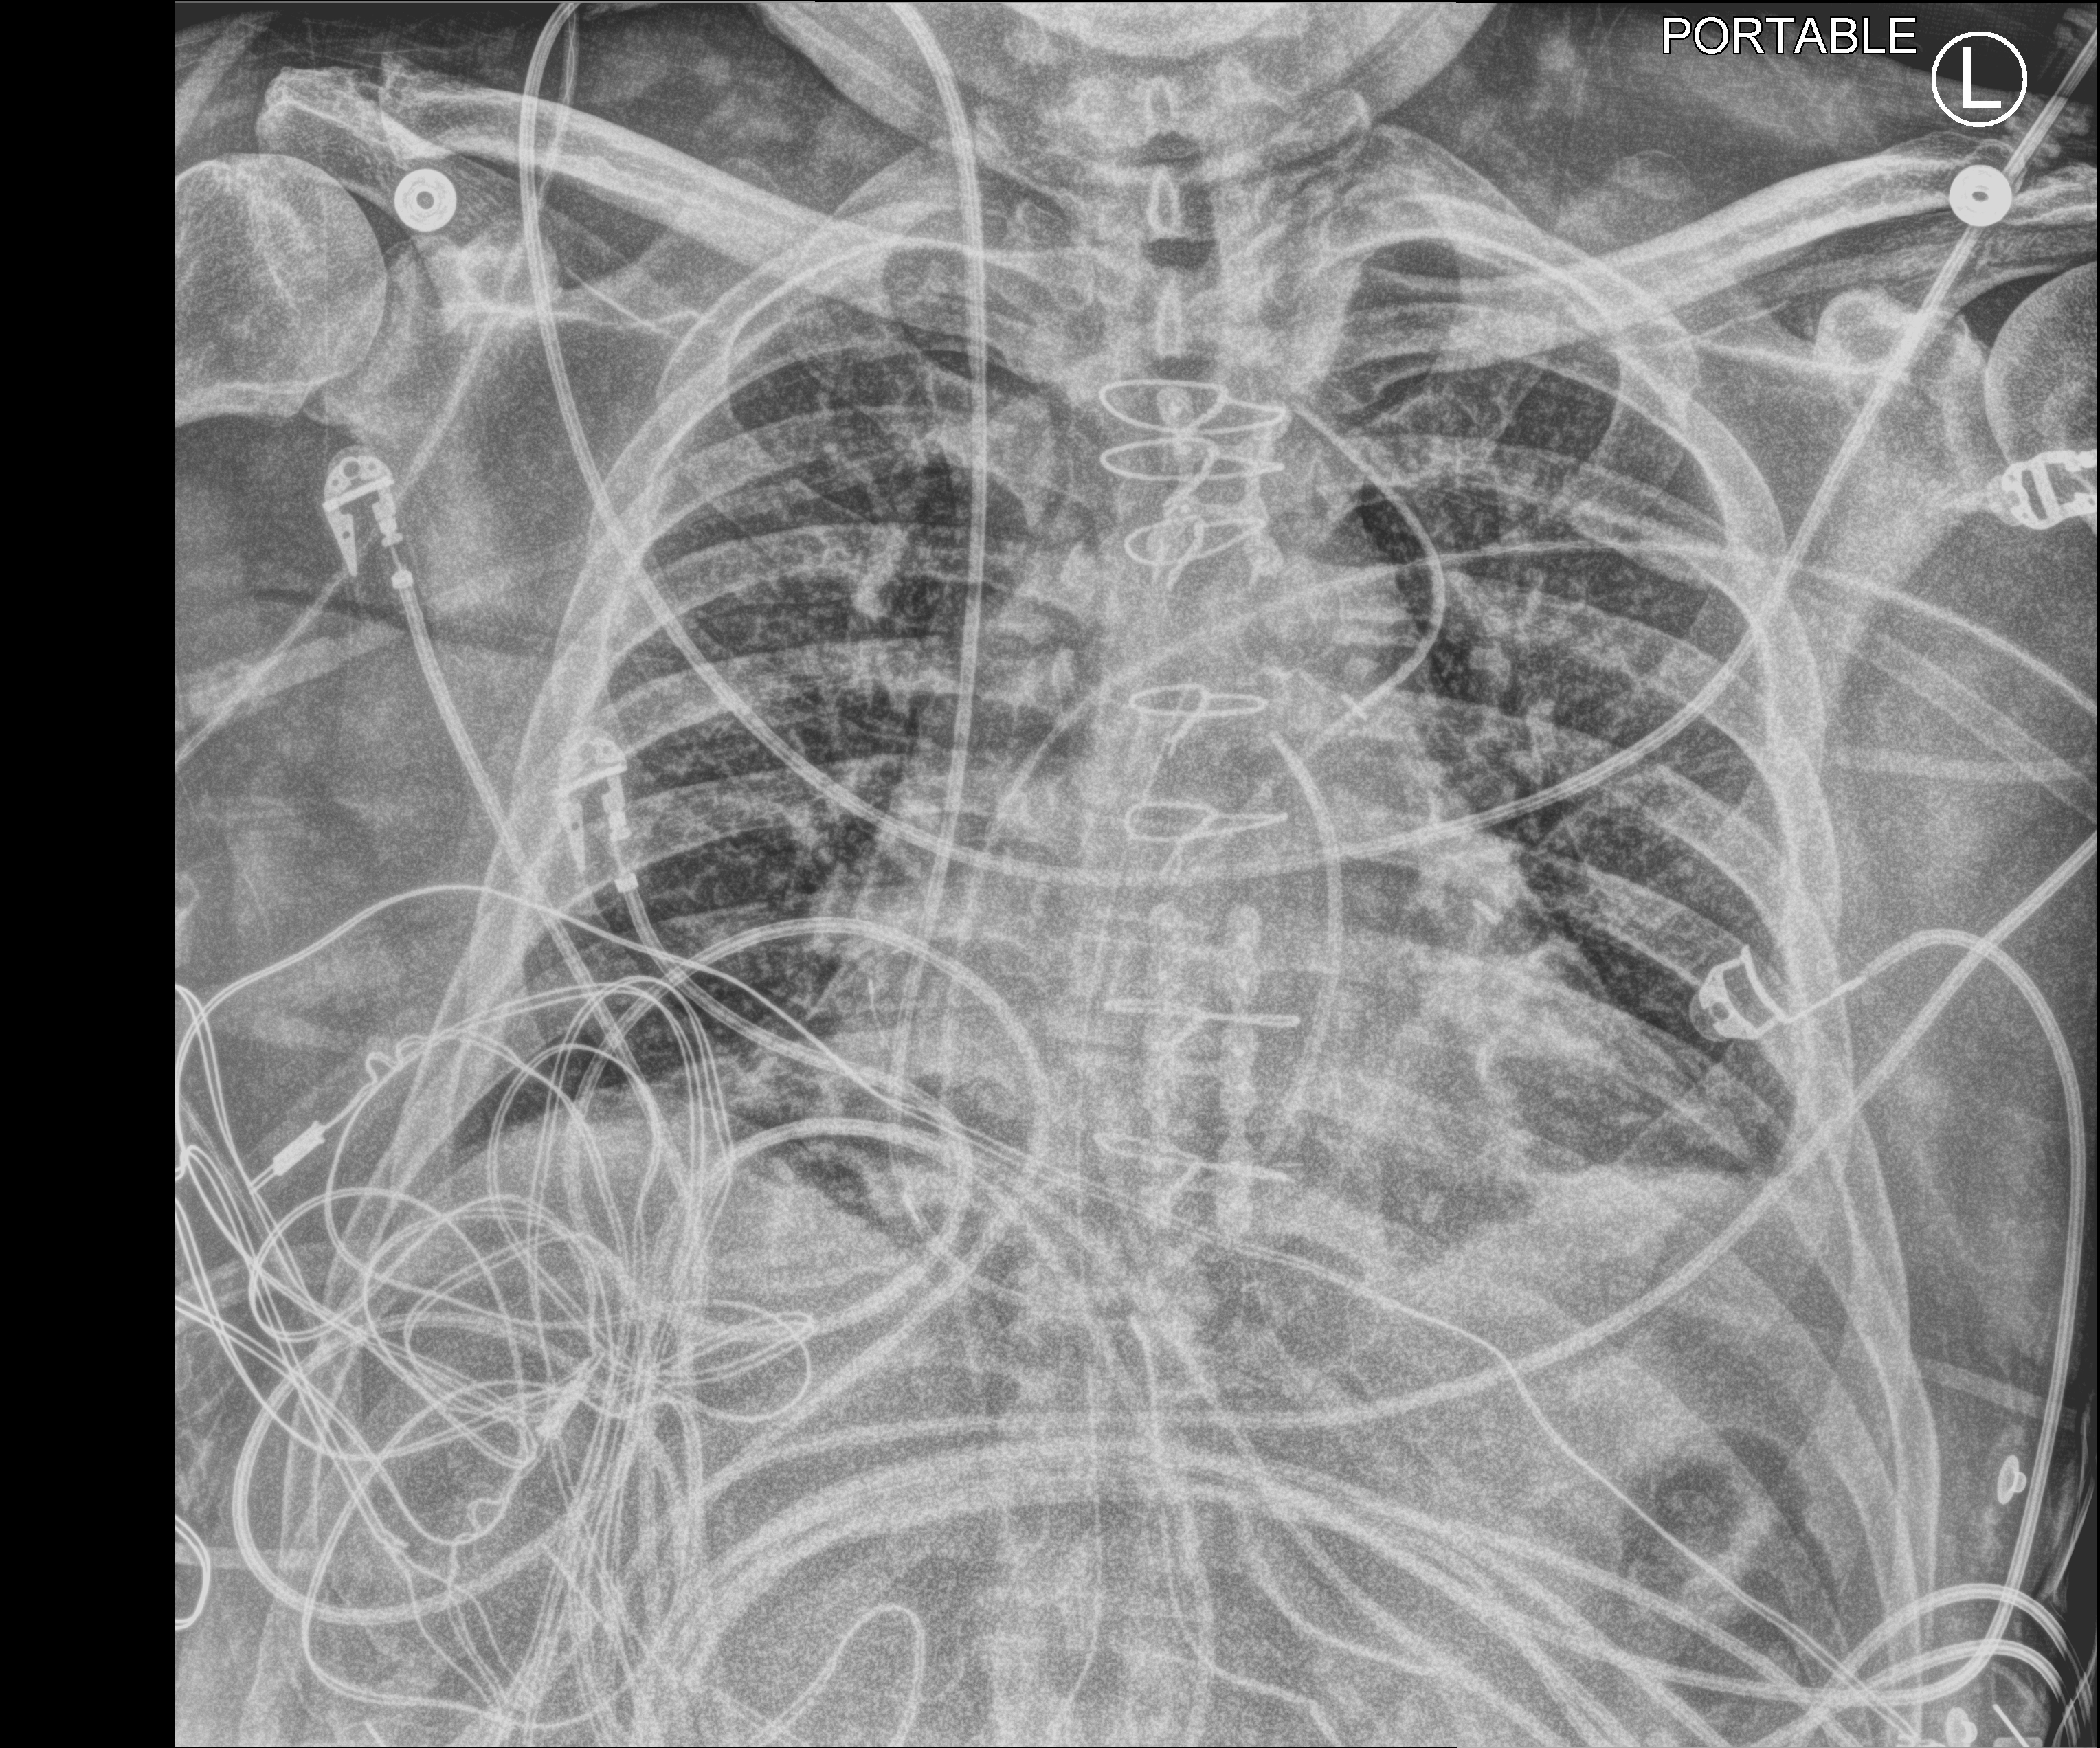
Chest X-ray (portable), anteroposterior (AP) projection. Patient hospitalised with COVID-19; male, aged 60–74 years.
From the hospital-stay record, not from the radiograph (when in the stay this image was taken is not recorded): length of hospital stay: 4 days; mechanically ventilated during this hospital stay: no; chronic kidney disease (admission record): no.